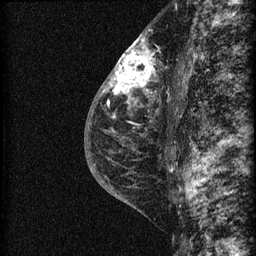
Breast MRI (dynamic contrast-enhanced), one sagittal slice. Slice 39 of 60 in the series (ordered by position). Dynamic contrast-enhanced series, image 2 of 3 at this slice position (ordered by acquisition). 1.5 T. TE 4.2 ms, TR 22.7 ms. 256 × 256 image matrix, field of view 180 × 180 mm. Female patient, age 48 years. Case-level facts recorded for this patient, not image findings: setting: breast cancer imaged before/during neoadjuvant chemotherapy; receptor status: triple-negative.
Outlined on this slice (semi-automatic segmentation, software-assisted and operator-edited):
- analysis volume of interest (the breast-tissue region the enhancement analysis was run in; not a lesion): bounding box [x1, y1, x2, y2] px = [115, 34, 169, 162]
- tumour enhancement mask (voxels above the 90 % enhancement threshold inside the analysis volume of interest): [115, 36, 155, 103]